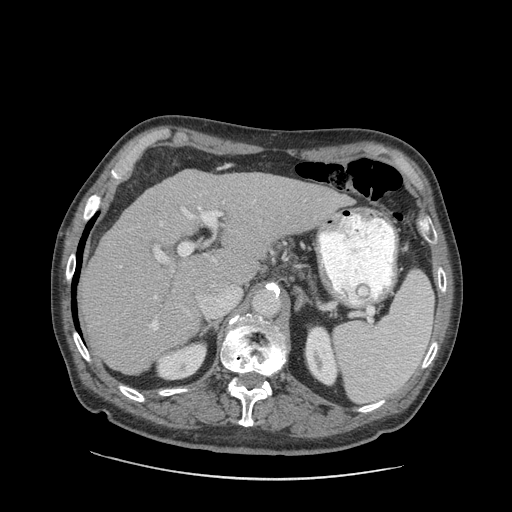
Contrast-enhanced abdominal CT (liver protocol), one axial slice; slice 57 of 89 in the series (ordered by position); reconstruction kernel STANDARD; soft-tissue window (W 400 / L 40 HU); 512 × 512 image matrix, field of view 420 × 420 mm. From the clinical record (not read from this slice): diagnosis: hepatocellular carcinoma (patient treated with transarterial chemoembolisation; whether this scan precedes or follows treatment is not stated here); TNM stage (as recorded): Stage-I; Child-Pugh class: A.
Structures marked on this image (semi-automatic segmentation, software-assisted and operator-edited):
- liver parenchyma outside the tumour (the mass and vessels are separate outlines, so this box may not span the whole liver): bounding box [x1, y1, x2, y2] px = [80, 170, 350, 374]
- liver vessels: [119, 194, 306, 330]